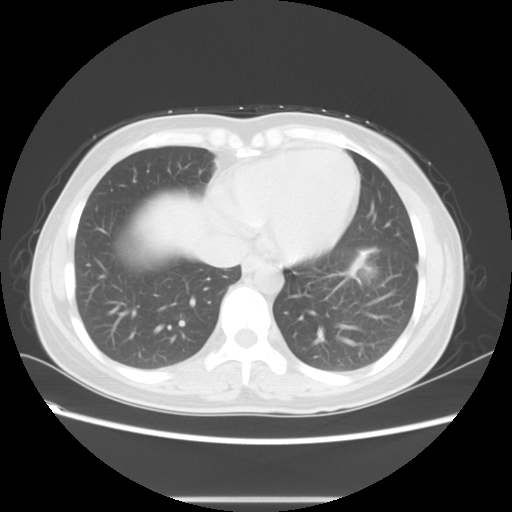
Chest CT, one axial slice; slice 20 of 56 in the series (ordered by position); reconstruction kernel STANDARD; lung window (W 1500 / L -600 HU); 5 mm slice thickness; 512 × 512 image matrix, field of view 350 × 350 mm. Female patient, age 41 years. Case-level facts recorded for this patient, not image findings: clinical TNM (as recorded): T1c N3 M1b.
Outlined on this slice (rectangle marked by the reading radiologist):
- lung tumour (recorded histology: adenocarcinoma): box from (x=348, y=239) to (x=388, y=285) px